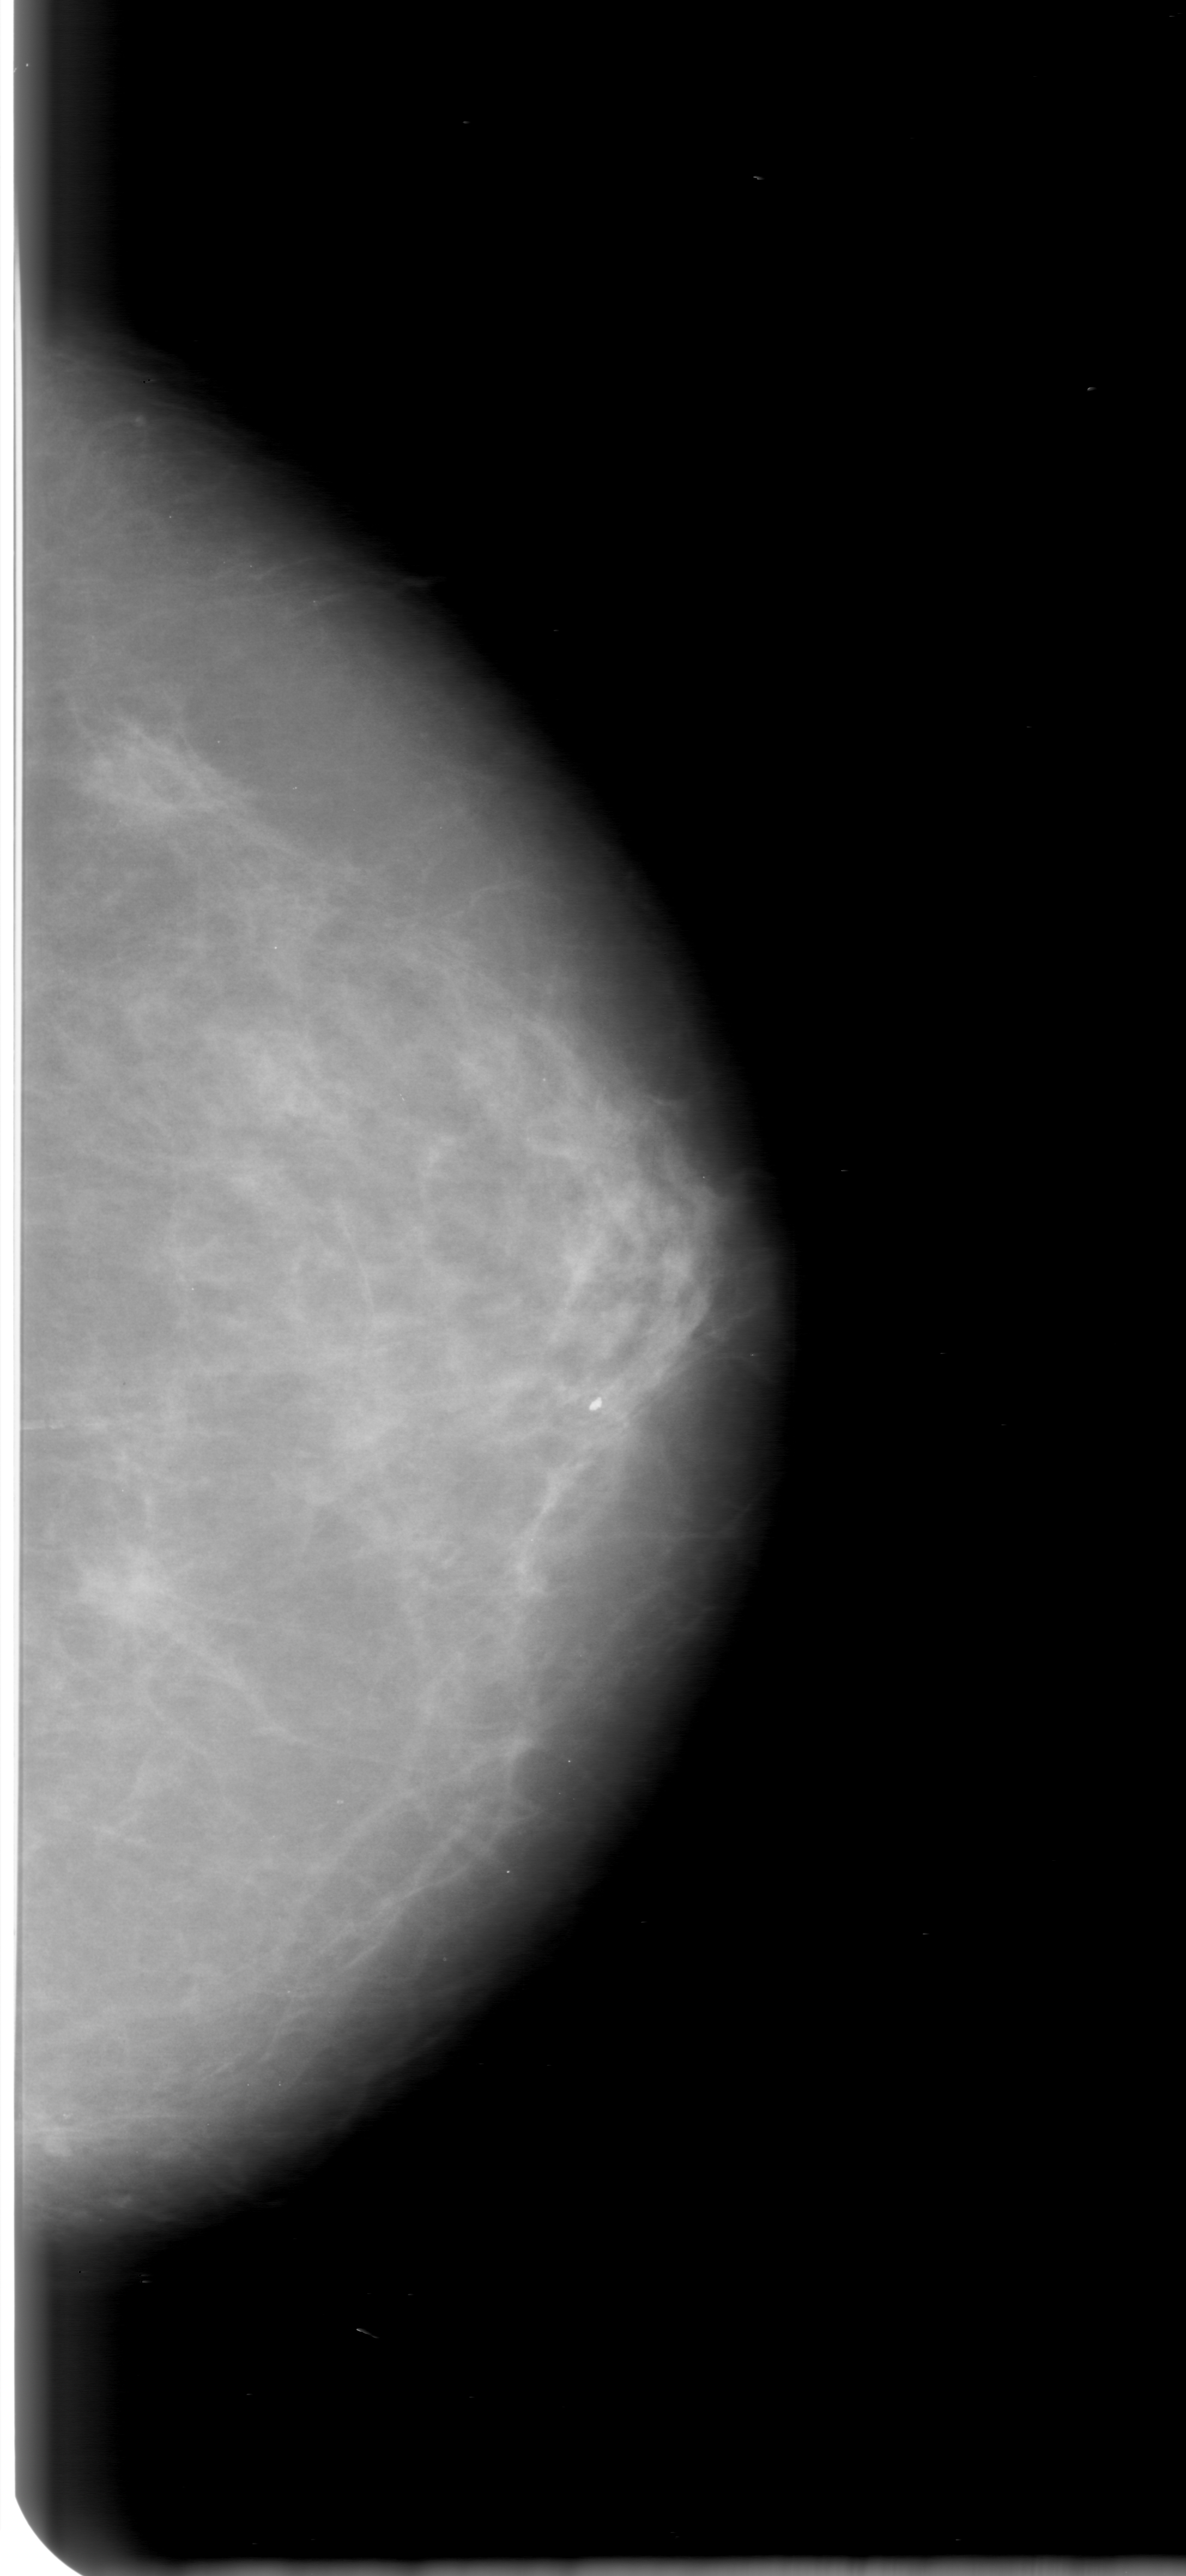
Scanned film-screen mammogram, left breast, CC view, BI-RADS breast density category 2 (scale 1–4).
- Mass, shape irregular, margins ill defined; BI-RADS assessment category 2; subtlety rating 3 on a 1 (subtle) to 5 (obvious) scale; pathology result (as recorded, not read from the image): benign.